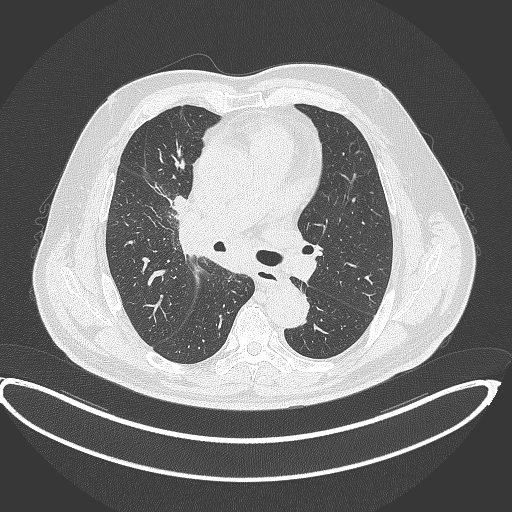
Chest CT, one axial slice. Position 242 of 390 along the scan axis. Reconstruction kernel B70f. Lung window (W 1500 / L -600 HU). 512 × 512 image matrix, field of view 448 × 448 mm. Patient: male, 62 years. Case-level facts recorded for this patient, not image findings: clinical TNM (as recorded): T1c N3 M1c.
Annotated regions visible in this slice (rectangle marked by the reading radiologist):
- lung tumour (recorded histology: adenocarcinoma): bounding box (x1, y1, x2, y2) in pixels: (169, 193, 189, 218)